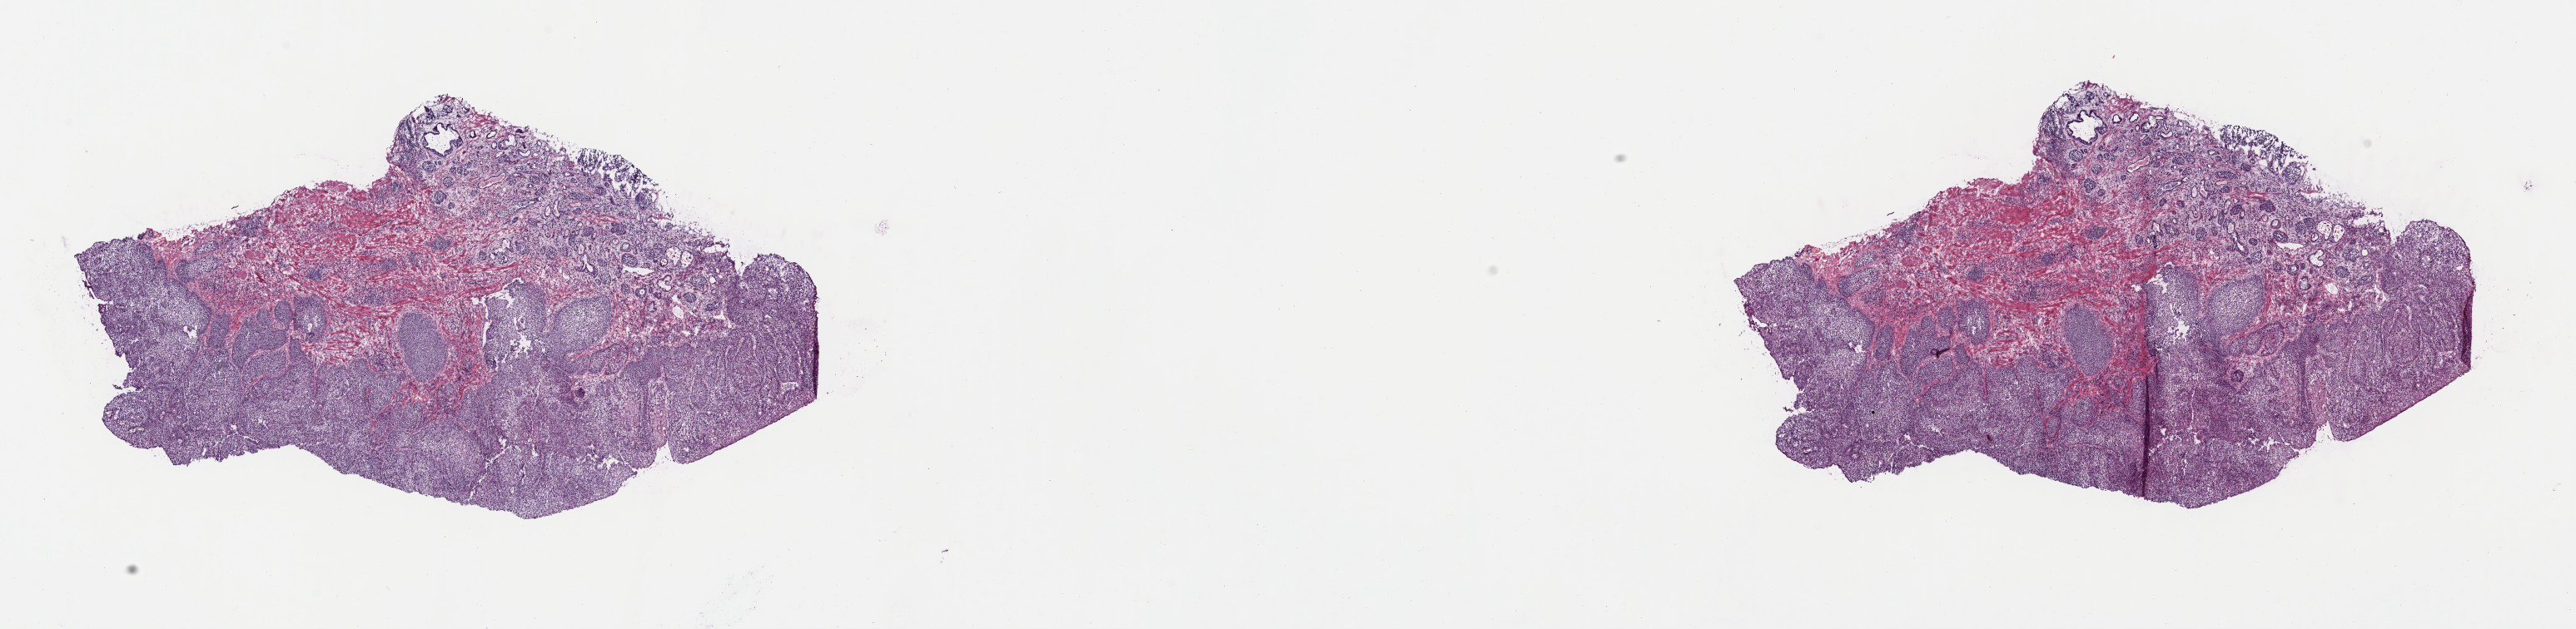
Hematoxylin and eosin (H&E) stained whole-slide image — low-resolution overview of the scanned area, about 24.4 x 6.0 mm (acquisition: 40x scan); frozen section from the top of the tissue portion; primary tumour sample from the esophagus. Female patient; age at initial diagnosis 54 years. Histologic grade: GX (grade cannot be assessed). Pathologist review of this section (percent, as recorded): tumour cells 100%, tumour nuclei 70%, normal cells 0%, stromal cells 0%, necrosis 0%. Infiltration values recorded for this section: lymphocyte infiltration 5%, monocyte infiltration 0%, neutrophil infiltration 1%.
• pathologic diagnosis: Basaloid squamous cell carcinoma (lower third of esophagus)
• TNM: T1 N0
• lymph nodes positive (case pathology): 0 of 3 examined
• AJCC pathologic stage: IA (7th edition)